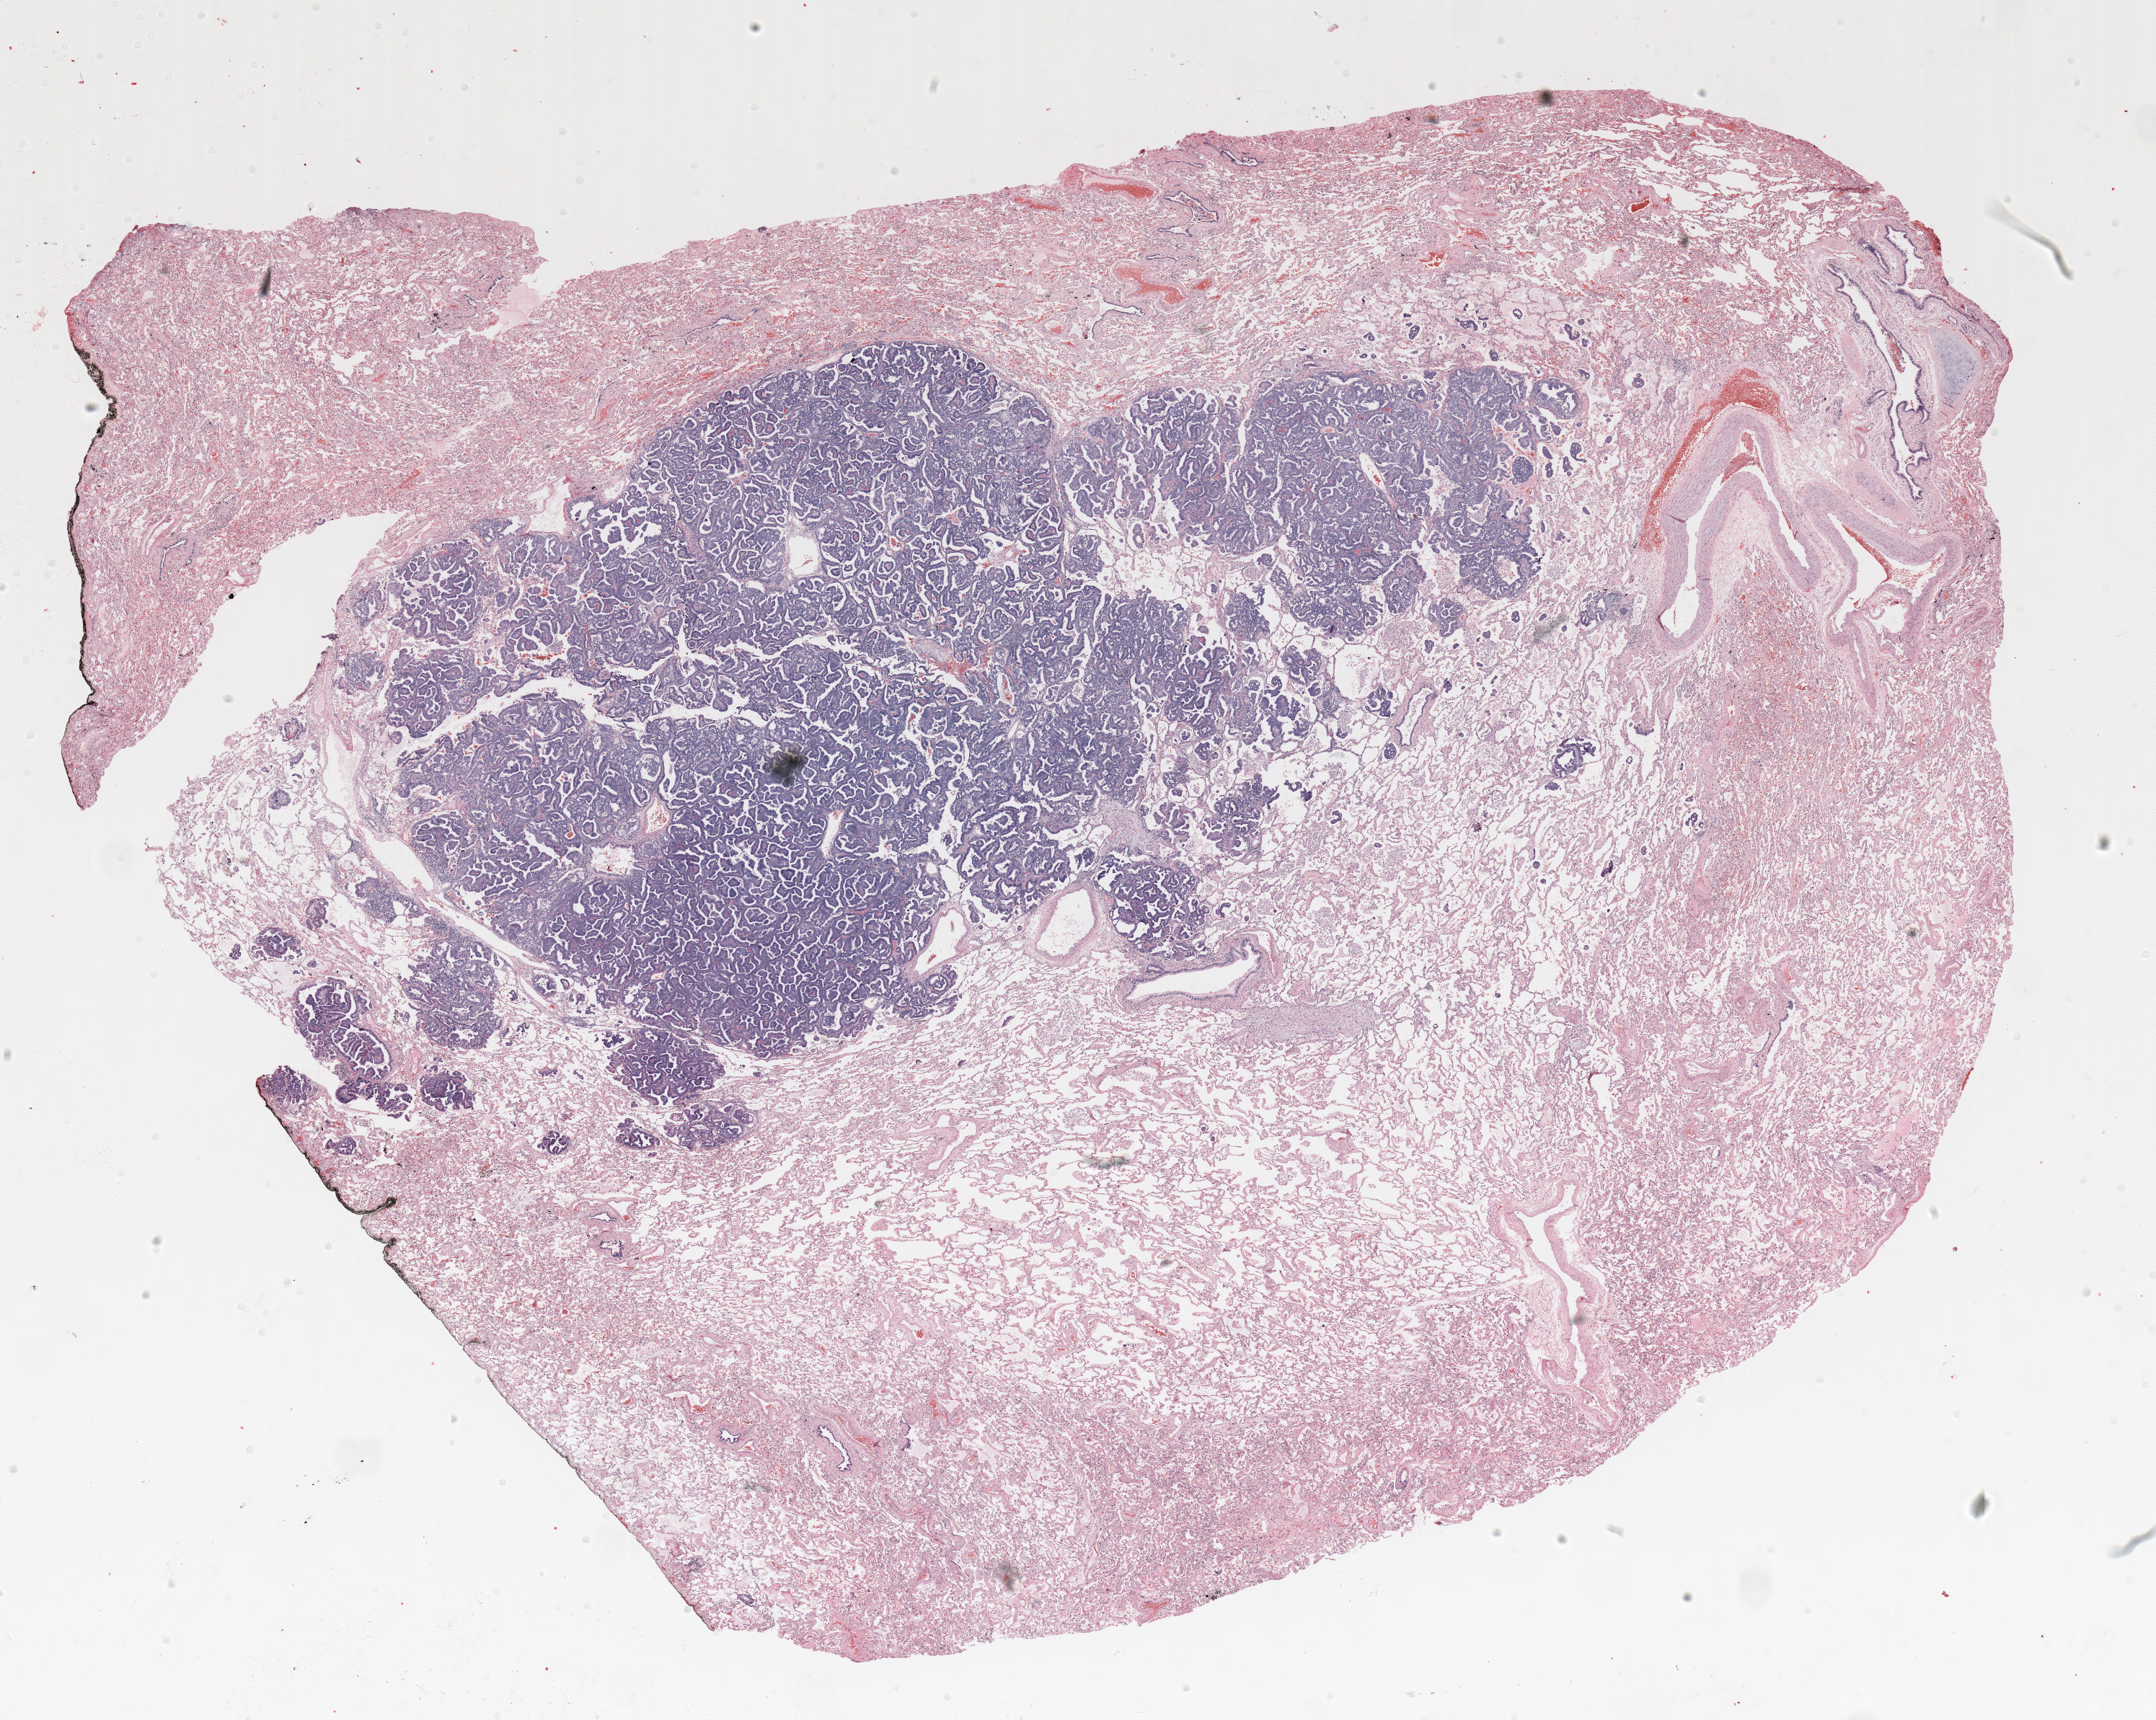
H&E whole-slide image, low-resolution overview of the scanned area, about 24.0 x 19.2 mm, FFPE section, lung. Female, age 67 at enrolment. Former smoker at enrolment. Grade: moderately differentiated (G2).
ICD-O-3 topography: upper lobe of lung (C34.1). Participant's lung-cancer diagnosis: Adenocarcinoma, NOS. Primary tumour location (clinical record): left upper lobe. Stage (AJCC 6th edition): IIA. Tumour size (pathology): 23 mm.